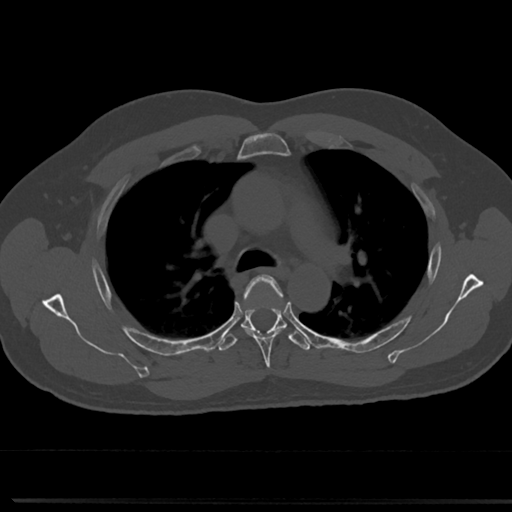
CT including the spine, one axial slice. Slice 523 of 817 in the series (ordered by position). Reconstruction kernel Br40s/3. Bone window (W 1800 / L 400 HU). 512 × 512 image matrix, field of view 355 × 355 mm. Patient: male, 61 years. From the clinical record (not read from this slice): primary cancer: prostate.
Outlined on this slice (semi-automatically segmented with operator editing):
- T4 vertebra: bounding box (x1, y1, x2, y2) in pixels: (239, 275, 288, 361)
- T5 vertebra: (224, 309, 310, 349)